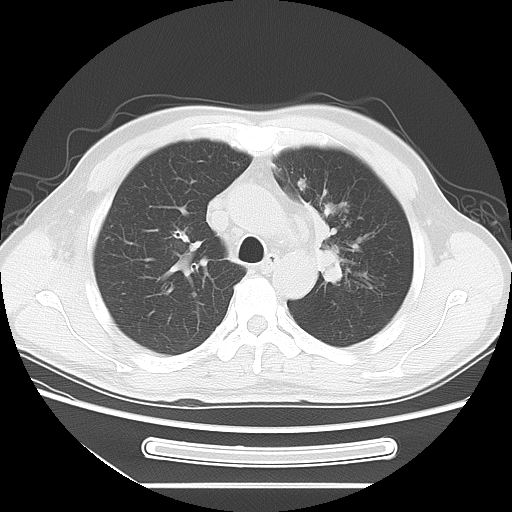
Chest CT, one axial slice. Position 51 of 71 along the scan axis. Reconstruction kernel LUNG. 120 kVp. Lung window (W 1500 / L -600 HU). 512 × 512 image matrix, field of view 366 × 366 mm. Patient: male, 51 years. From the clinical record (not read from this slice): clinical TNM (as recorded): T1c N3 M0.
Outlined on this slice (rectangle marked by the reading radiologist):
- lung tumour (recorded histology: adenocarcinoma): bounding box (x1, y1, x2, y2) in pixels: (313, 196, 366, 291)